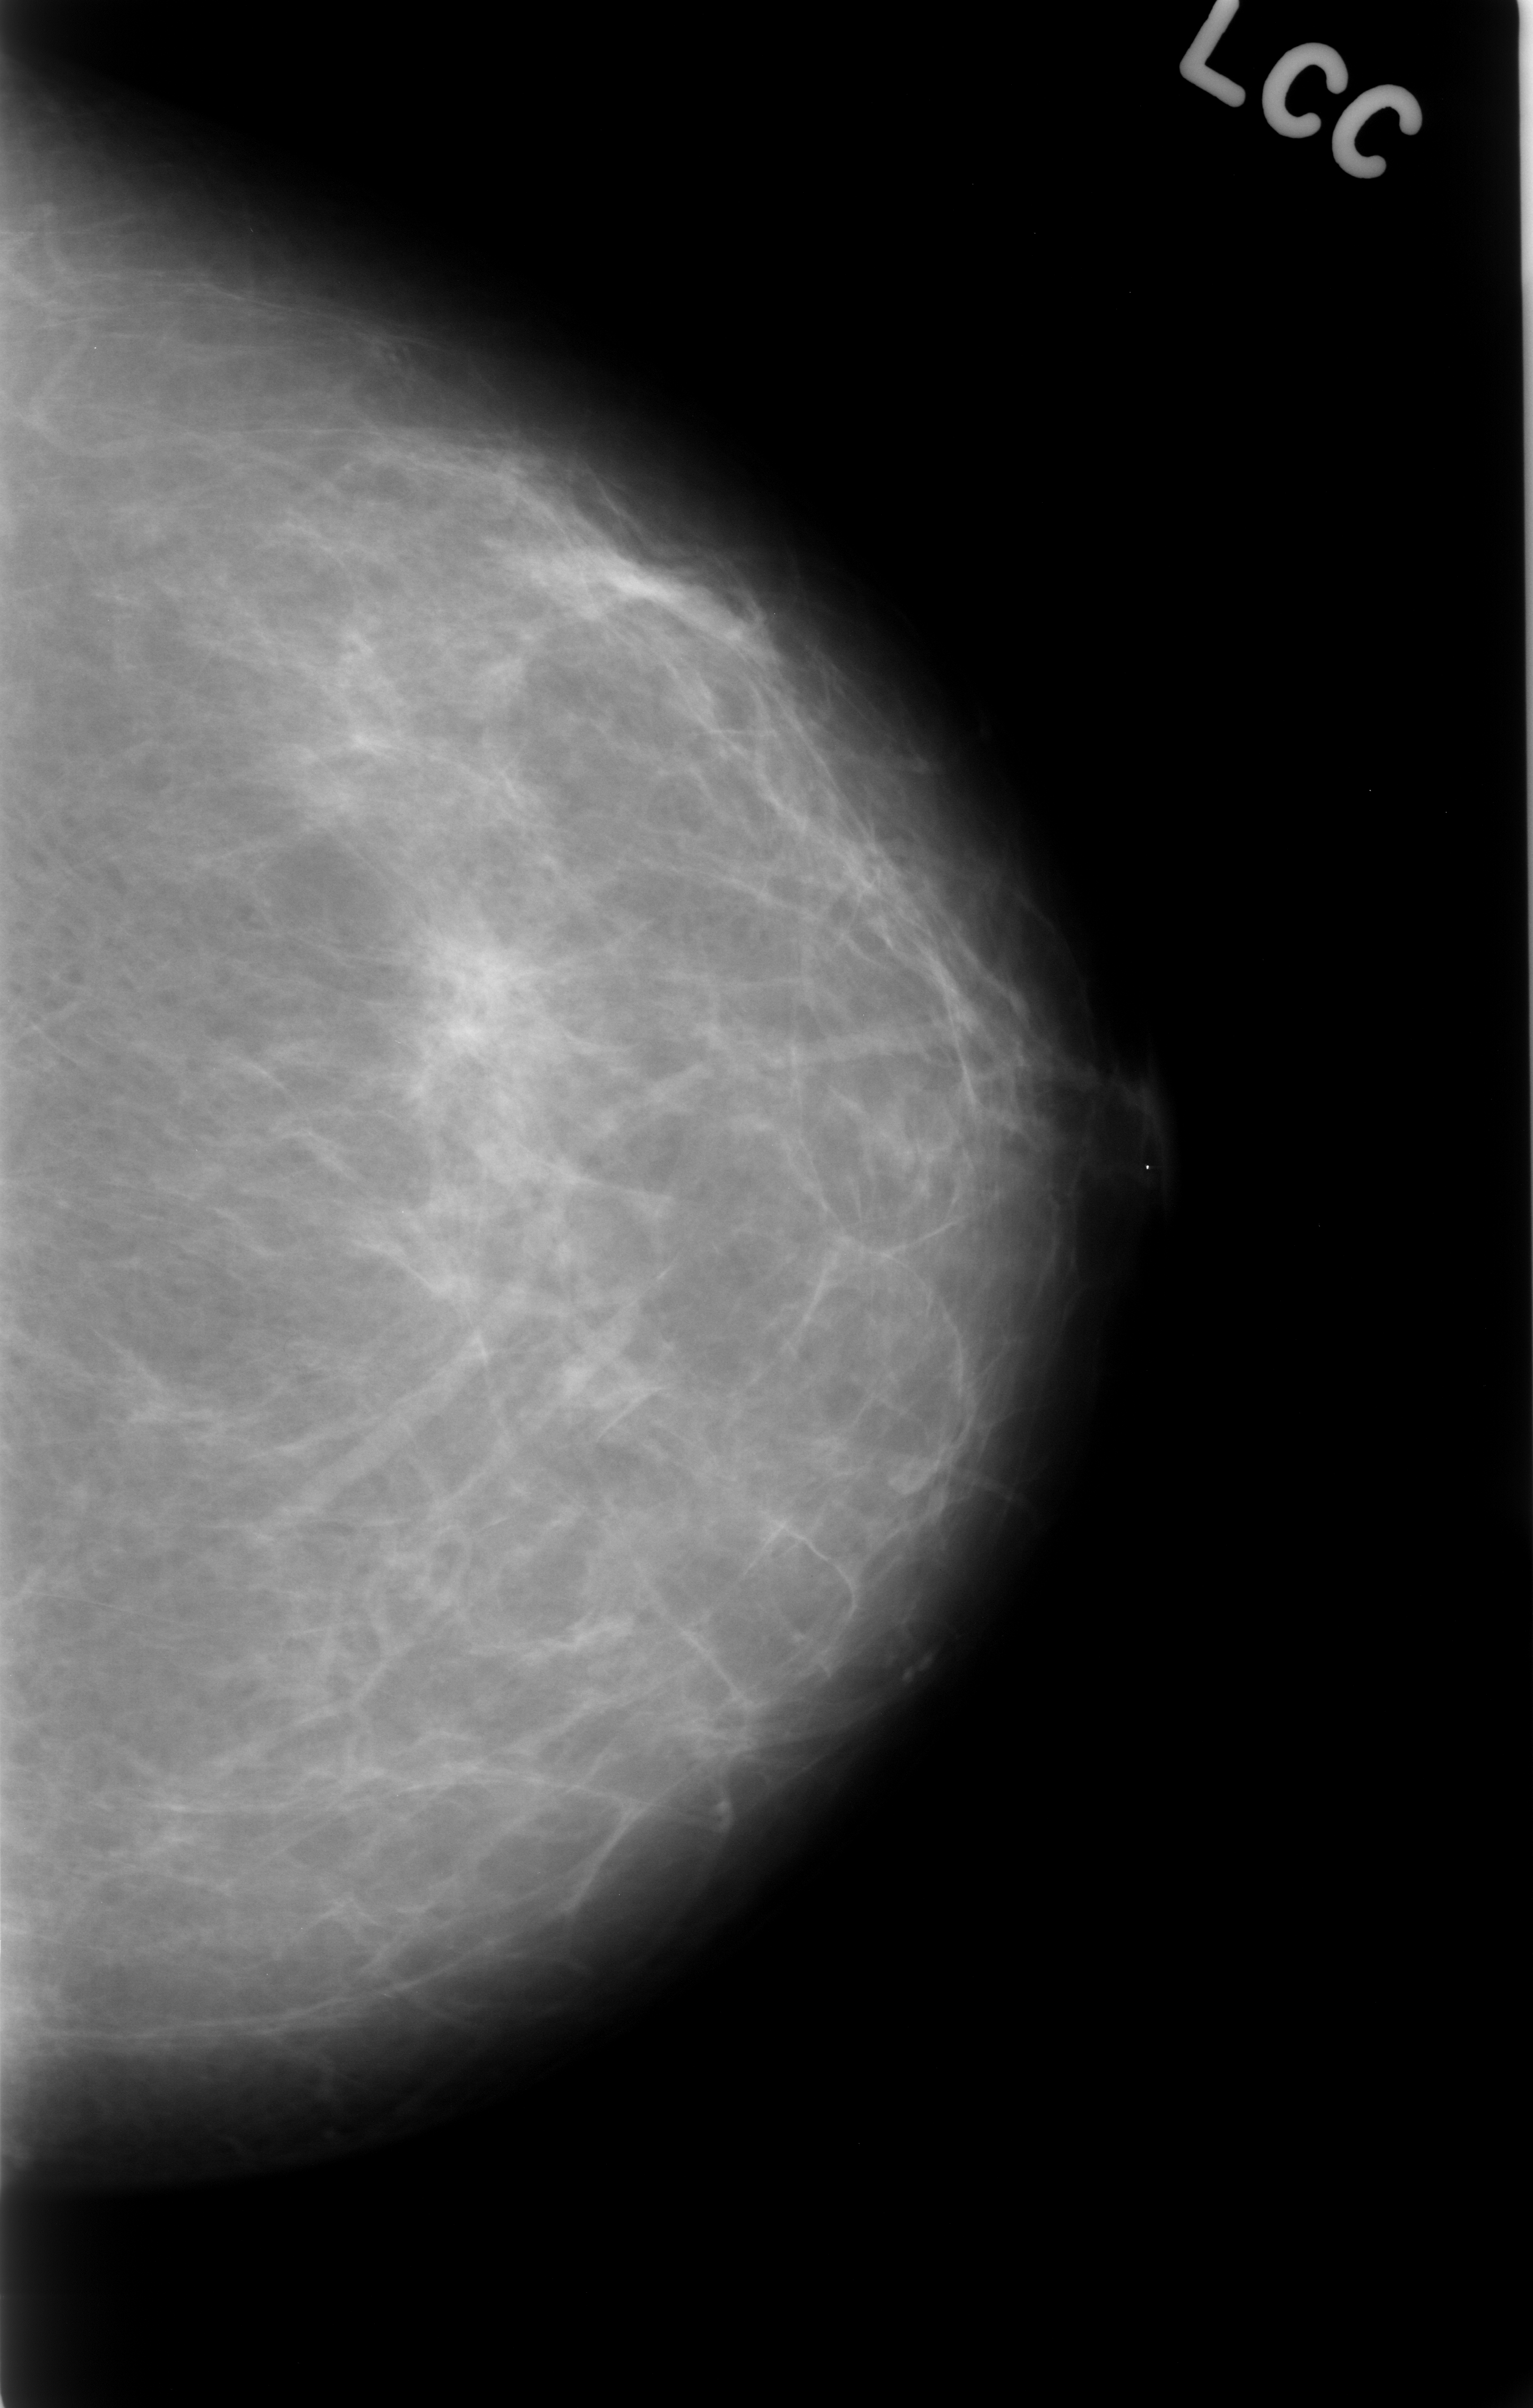
Scanned film-screen mammogram; left breast; craniocaudal (CC) view; BI-RADS breast density category 1 (scale 1–4).
Finding: mass, shape architectural distortion; BI-RADS assessment category 3; benign without callback (not worked up further).